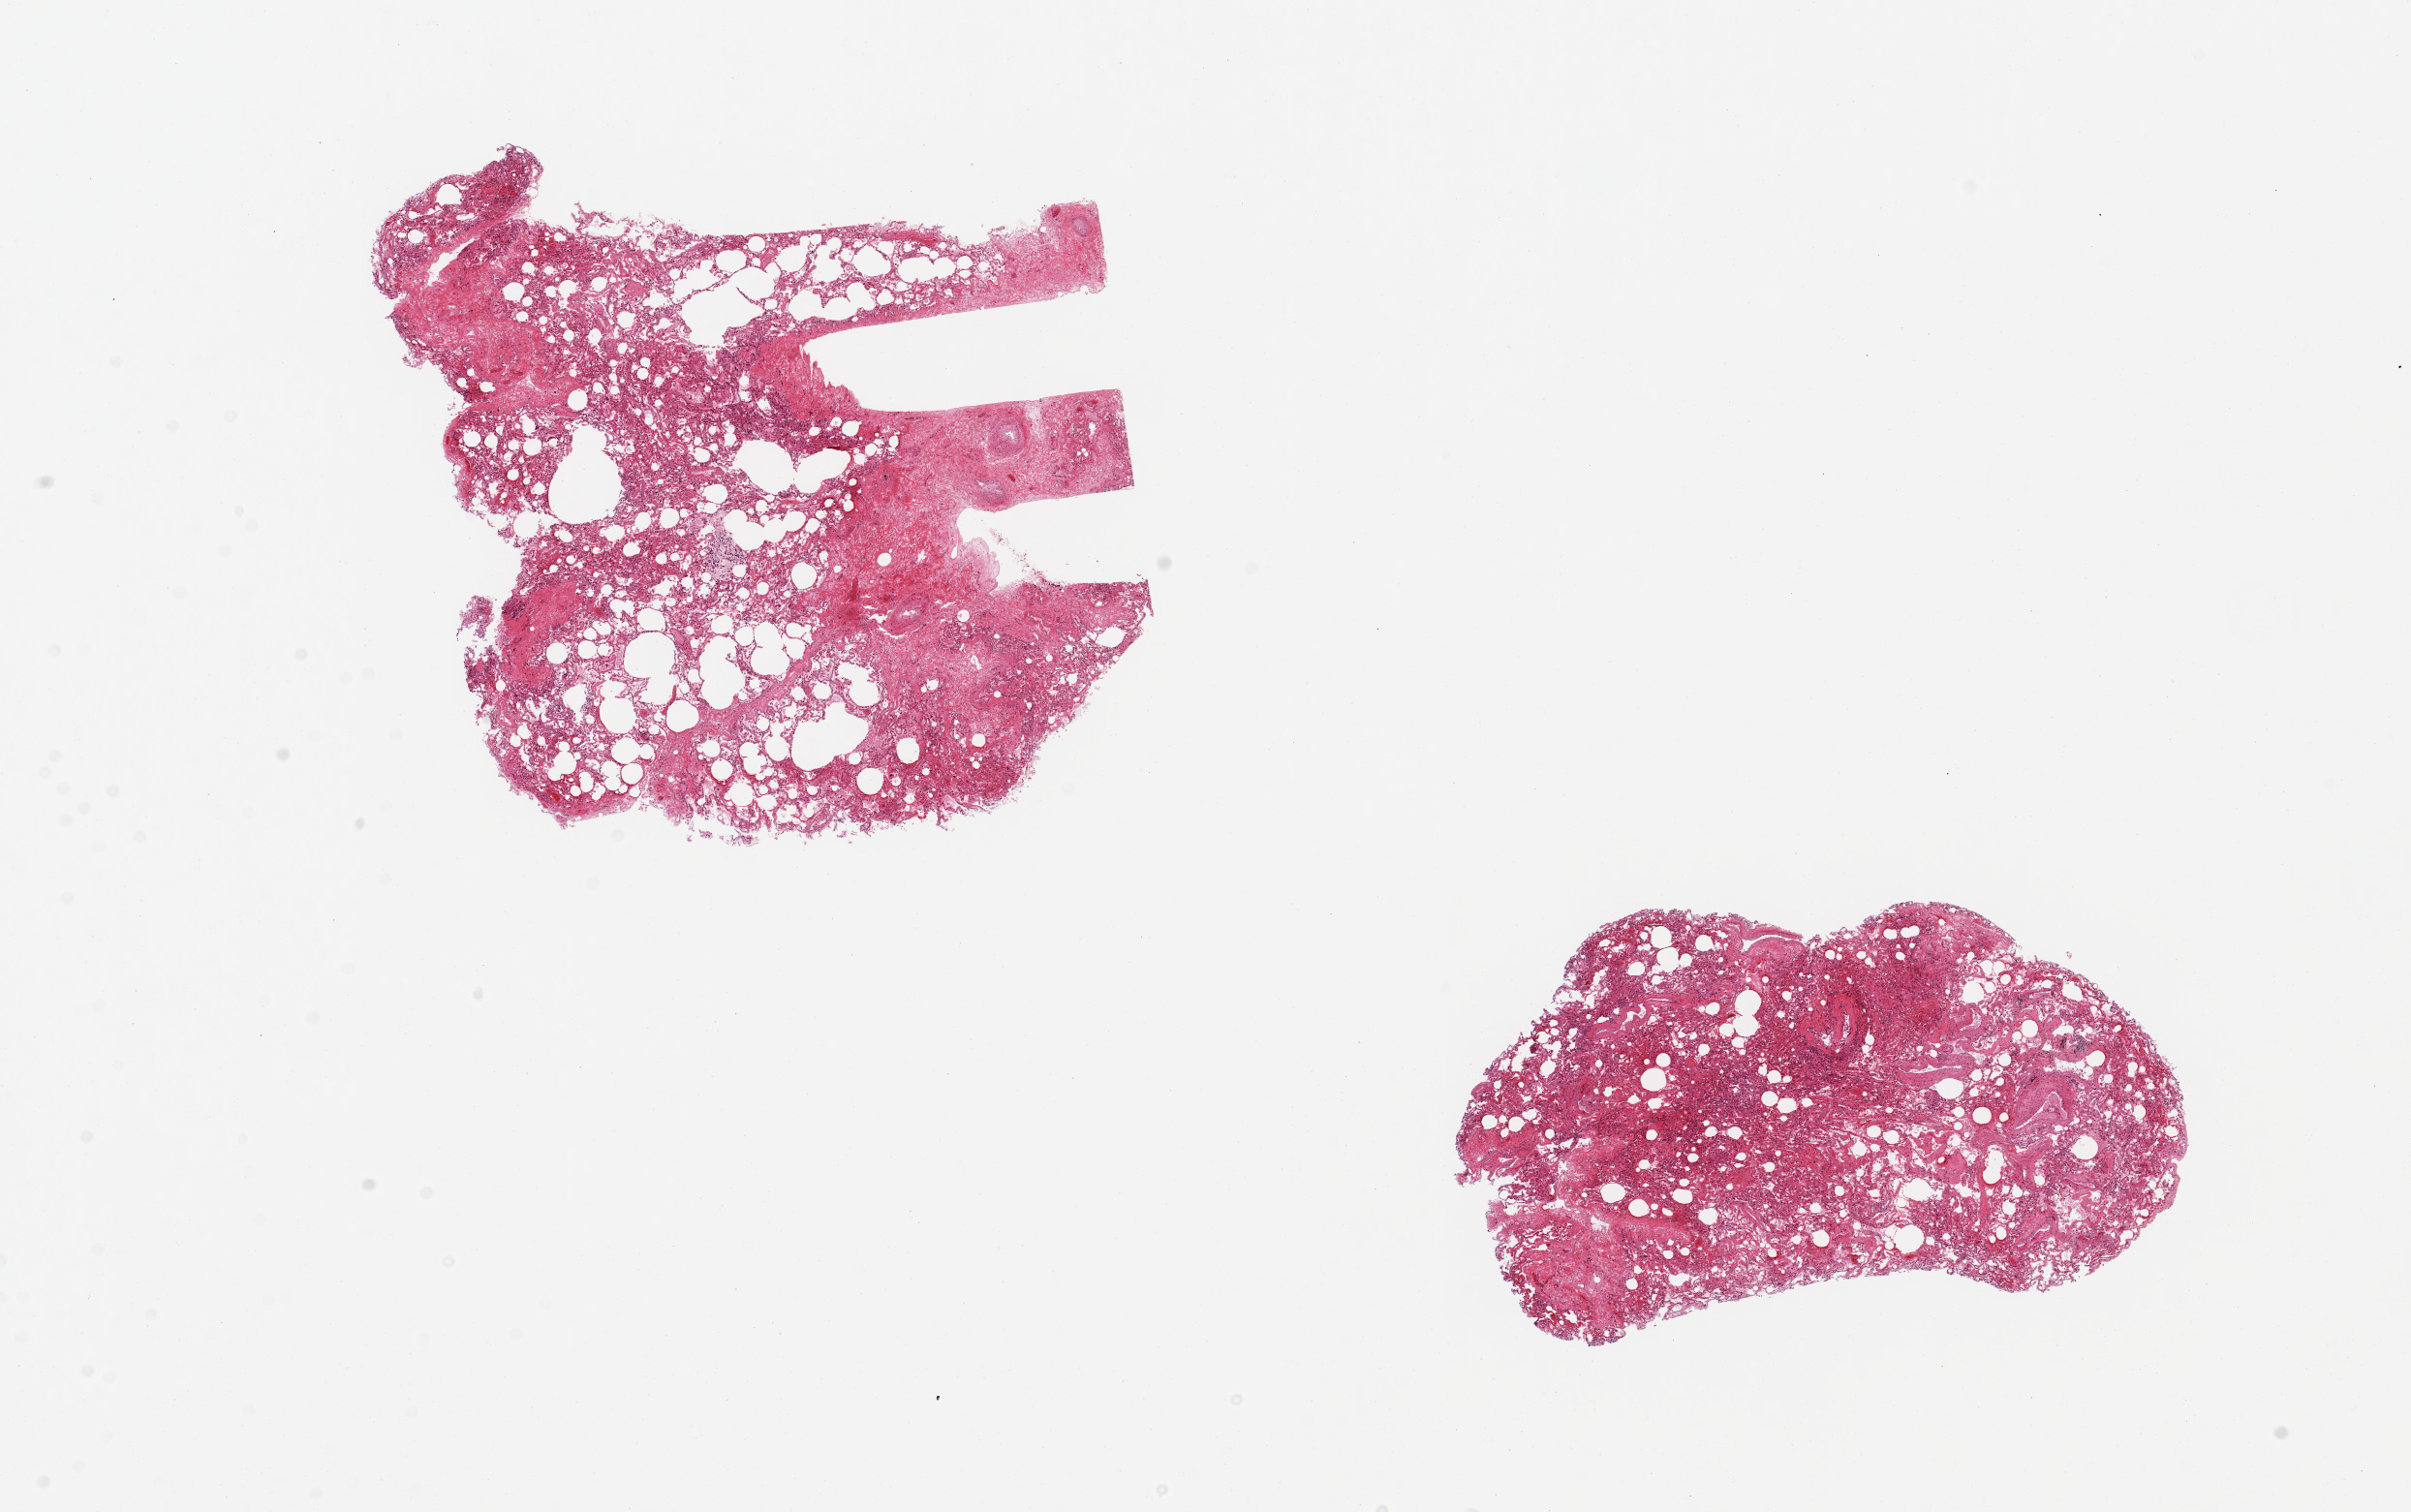
Hematoxylin and eosin (H&E) whole-slide image, brightfield, a low-resolution overview of the entire scanned area, about 19.7 x 12.3 mm; PAXgene-fixed, paraffin-embedded tissue; section of lung (target tissue); tissue donor sample. Donor sex: male.
Pathologist's review note for this sample: 2 pieces, 6x6 & 6x3mm.